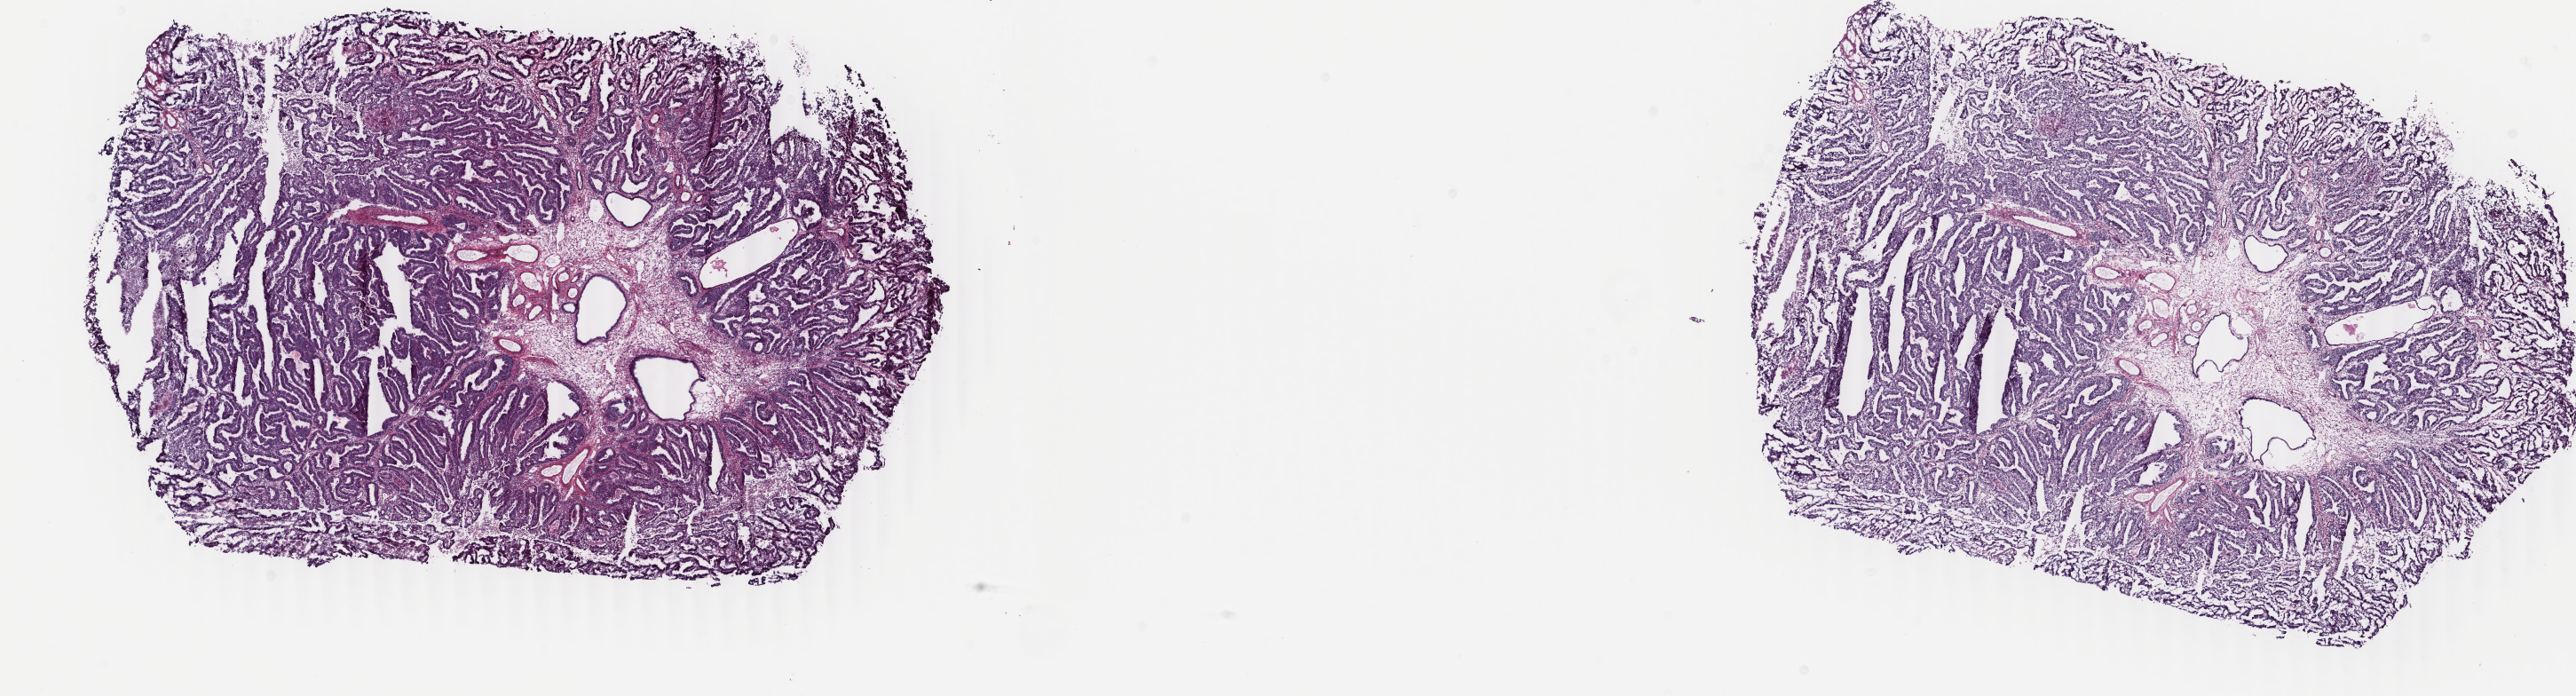
Whole-slide histology image, H&E-stained, low-resolution overview of the scanned area, about 23.1 x 6.2 mm, frozen section from the bottom of the tissue portion, sample: primary tumour, uterus. Patient: female, age at initial diagnosis 57 years. Histologic grade: G2 (moderately differentiated). Composition of this section per pathologist review: tumour cells 80%, tumour nuclei 90%, normal cells 0%, stromal cells 10%, necrosis 10%. Inflammatory infiltration, as recorded: lymphocyte infiltration 20%, monocyte infiltration 0%, neutrophil infiltration 10%.
• histologic diagnosis: Endometrioid adenocarcinoma, NOS (endometrium)
• FIGO stage: IB
• lymph nodes positive (case pathology): 0 of 48 examined